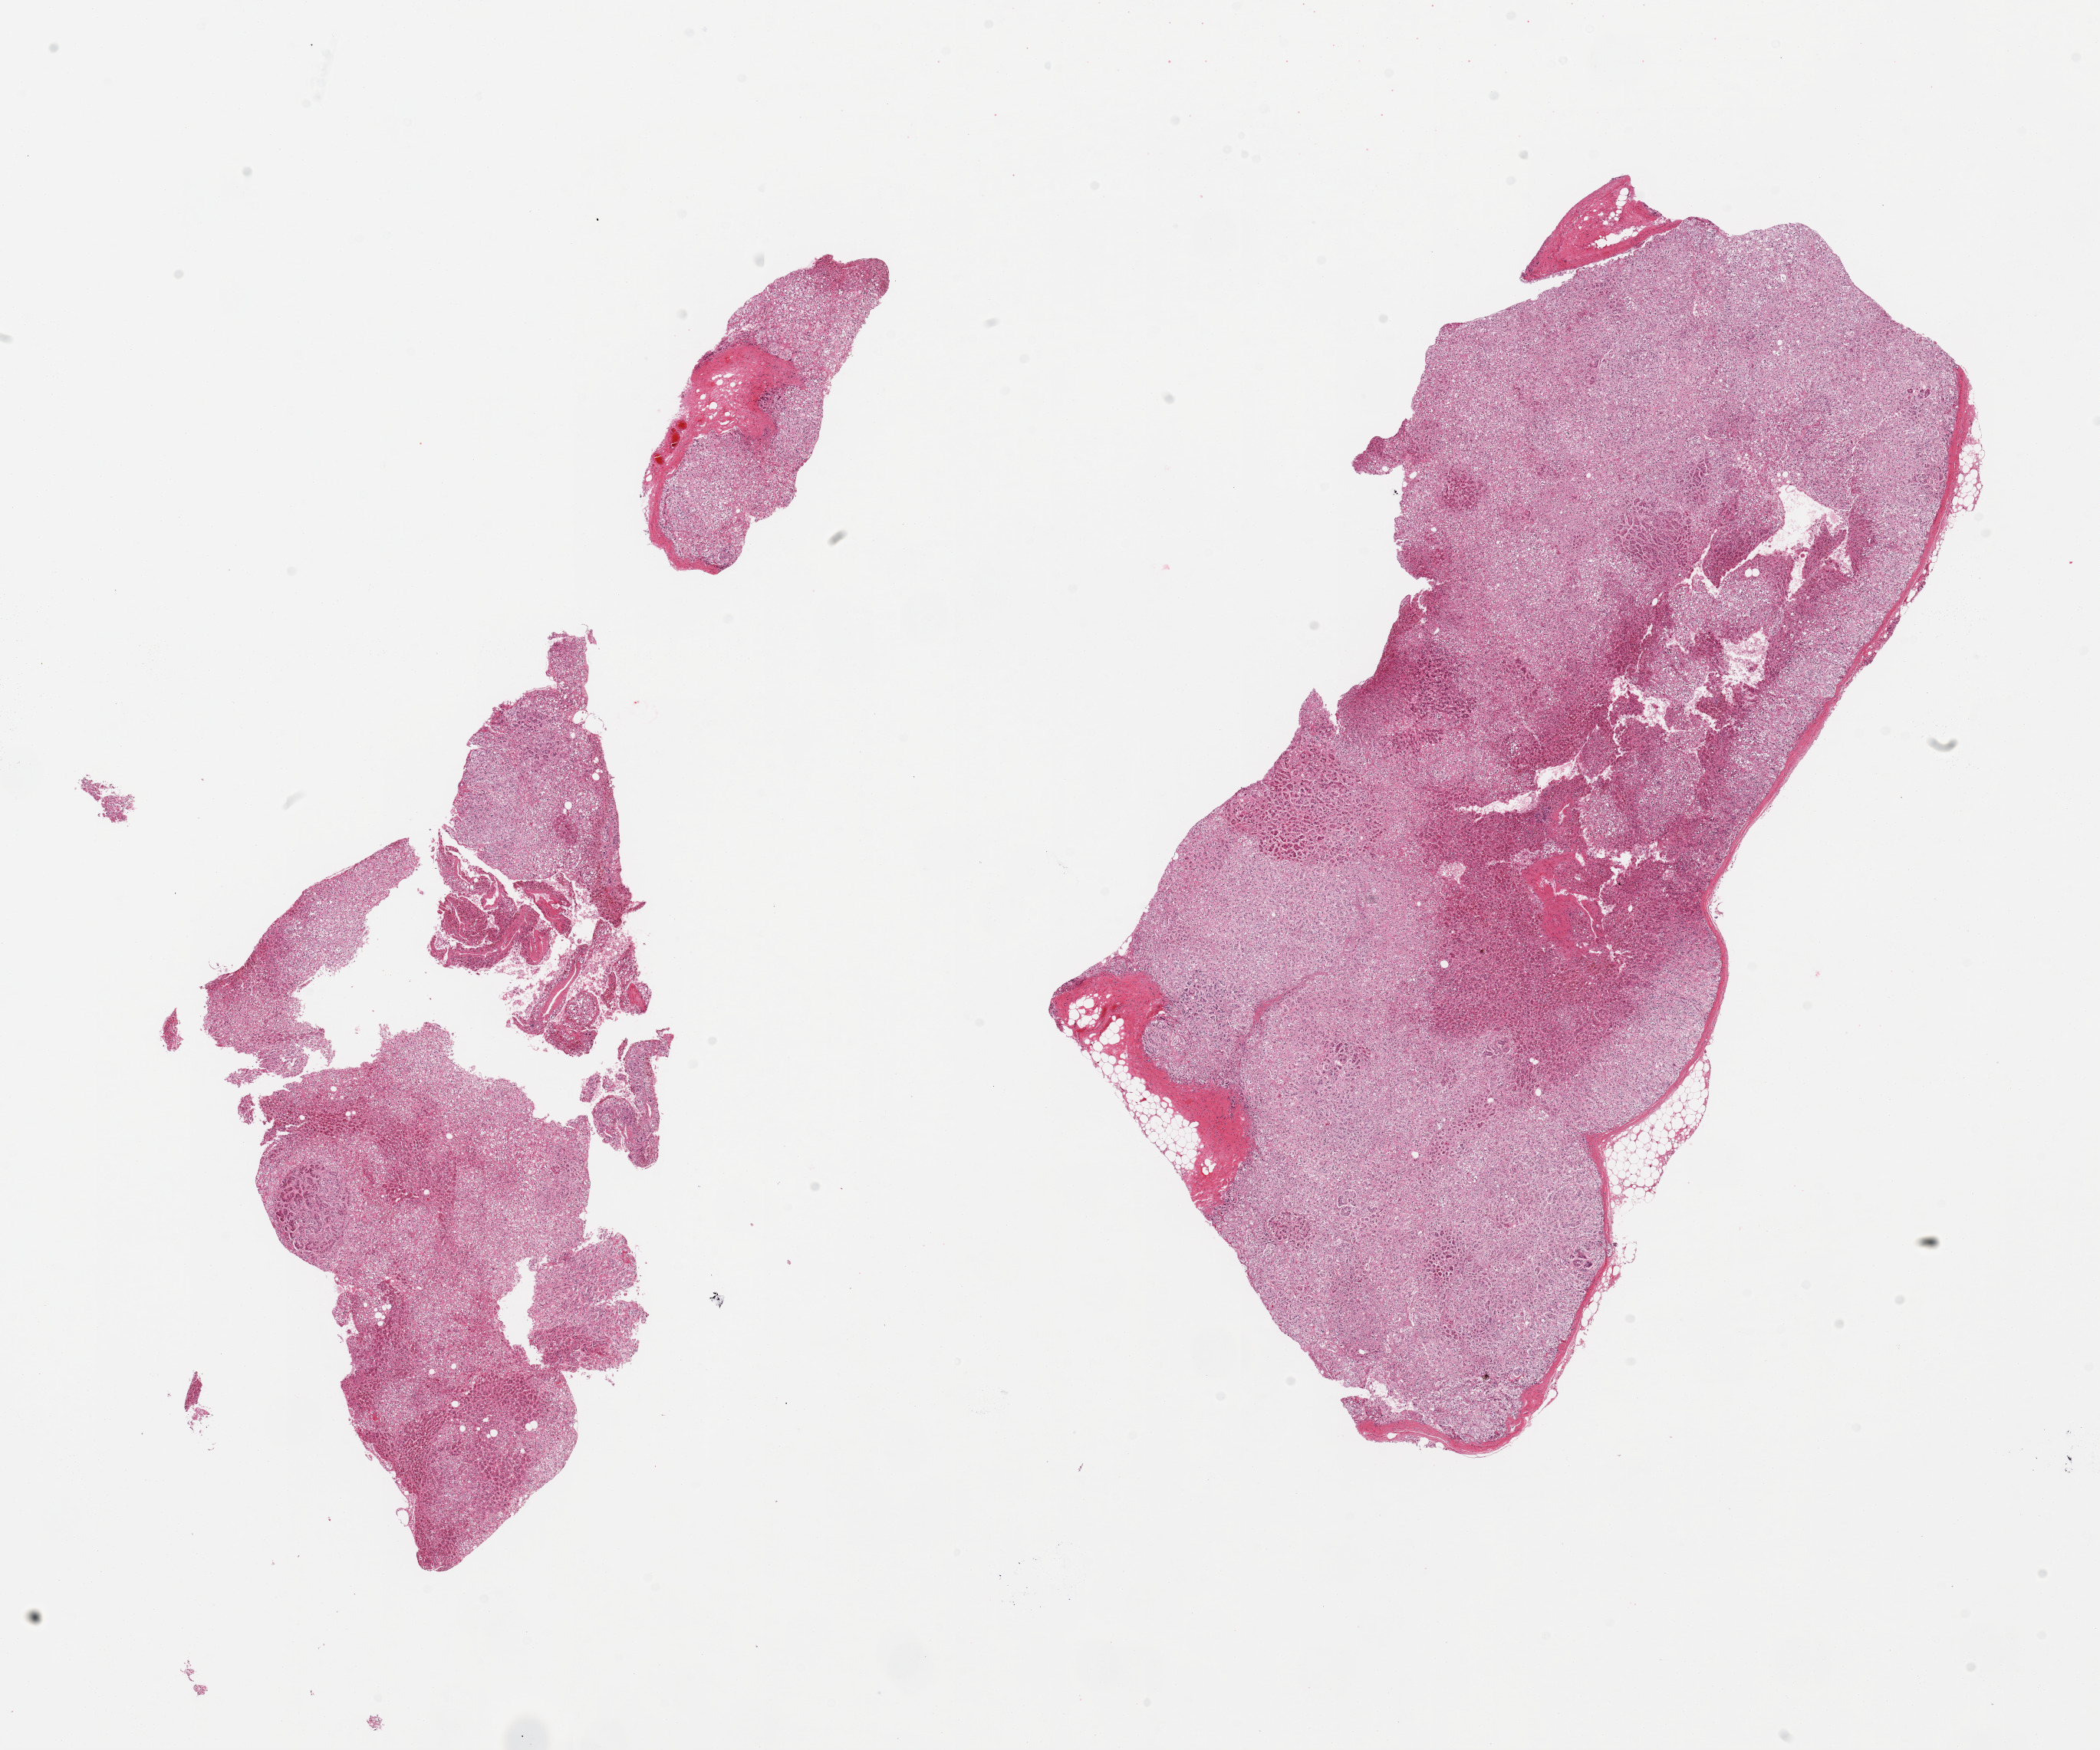
Whole-slide image, hematoxylin and eosin (H&E) stain, shown as a low-resolution overview of the whole scanned area (about 21.7 x 18.1 mm, slide scanned at 20x), PAXgene-fixed, paraffin-embedded tissue, section of adrenal gland (target tissue), donor tissue sample. Donor: male.
Reviewer comment on this tissue sample: 2 pieces, all cortex, trace fat.